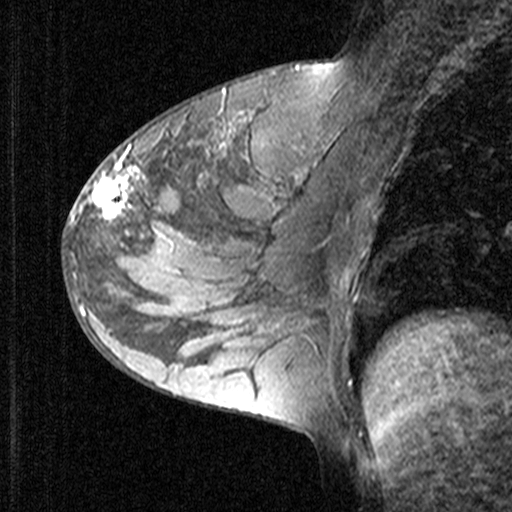
Breast MRI (dynamic contrast-enhanced), one sagittal slice. Dynamic contrast-enhanced study with each time point stored as its own series, time point 2 of 3 at this slice position (early post-contrast, ordered by acquisition time). 1.5 T. TE 4.5 ms, TR 11 ms. 3 mm slice thickness. 512 × 512 image matrix, field of view 200 × 200 mm. Female patient, age 27 years. Case-level facts recorded for this patient, not image findings: setting: breast cancer imaged before/during neoadjuvant chemotherapy; receptor status: HR-positive, HER2-negative.
Structures marked on this image (semi-automatic segmentation, software-assisted and operator-edited):
- analysis volume of interest (the breast-tissue region the enhancement analysis was run in; not a lesion): bounding box [x1, y1, x2, y2] px = [68, 146, 165, 239]
- tumour enhancement mask (voxels above the 90 % enhancement threshold inside the analysis volume of interest): [71, 146, 137, 222]